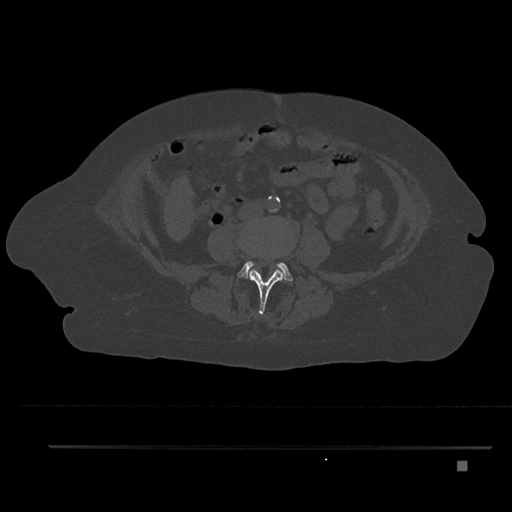
CT including the spine, one axial slice; position 108 of 797 along the scan axis; reconstruction kernel Br40s/3; 120 kVp; bone window (W 1800 / L 400 HU); 512 × 512 image matrix, field of view 437 × 437 mm. Patient: female, 76 years. Case-level facts recorded for this patient, not image findings: primary cancer: lung.
Annotated regions visible in this slice (semi-automatically segmented with operator editing):
- L3 vertebra: bounding box <250,268,285,314> (left, top, right, bottom; pixels)
- L4 vertebra: <238,239,292,281>